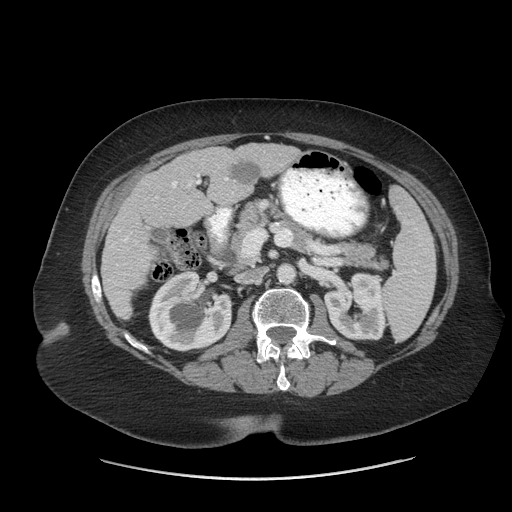
Contrast-enhanced abdominal CT (liver protocol), one axial slice; position 25 of 69 along the scan axis; reconstruction kernel STANDARD; soft-tissue window (W 400 / L 40 HU); 512 × 512 image matrix, field of view 420 × 420 mm. From the clinical record (not read from this slice): diagnosis: hepatocellular carcinoma (patient treated with transarterial chemoembolisation; whether this scan precedes or follows treatment is not stated here); TNM stage (as recorded): Stage-IIIB; Child-Pugh class: A; tumour differentiation: moderately differentiated; tumour nodularity: multinodular.
Annotated regions visible in this slice (semi-automatically segmented with operator editing):
- liver parenchyma outside the tumour (the mass and vessels are separate outlines, so this box may not span the whole liver): bounding box <100,142,300,318> (left, top, right, bottom; pixels)
- liver vessels: <123,174,228,242>